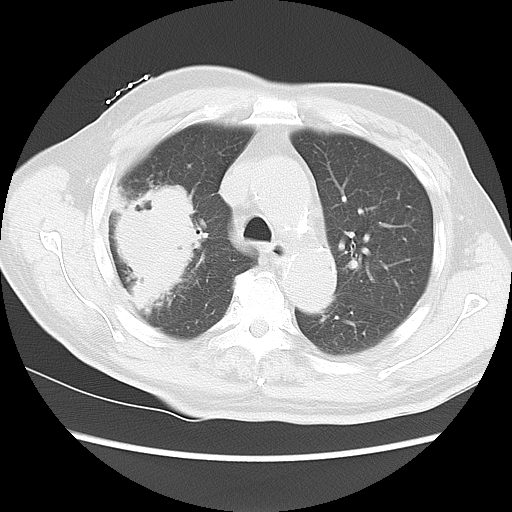
Chest CT, one axial slice; position 12 of 15 along the scan axis; 120 kVp; lung window (W 1500 / L -600 HU); 5 mm slice thickness; 512 × 512 image matrix, field of view 350 × 350 mm. Male patient, age 68 years. Case-level facts recorded for this patient, not image findings: clinical TNM (as recorded): T4 N3 M0.
Structures marked on this image (rectangle marked by the reading radiologist):
- lung tumour (recorded histology: squamous cell carcinoma): box from (x=113, y=190) to (x=204, y=320) px